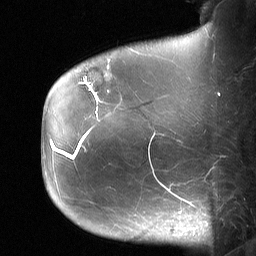
Breast MRI (dynamic contrast-enhanced), one sagittal slice; position 16 of 64 along the scan axis; dynamic contrast-enhanced study with each time point stored as its own series, time point 2 of 3 at this slice position (early post-contrast, ordered by acquisition time); 1.5 T; TE 4.8 ms, TR 27 ms; 256 × 256 image matrix, field of view 200 × 200 mm. Patient: female, 60 years. From the clinical record (not read from this slice): setting: breast cancer imaged before/during neoadjuvant chemotherapy; receptor status: HR-positive, HER2-negative.
Annotated regions visible in this slice (semi-automatically segmented with operator editing):
- analysis volume of interest (the breast-tissue region the enhancement analysis was run in; not a lesion): bounding box [x1, y1, x2, y2] px = [79, 50, 122, 99]
- tumour enhancement mask (voxels above the 90 % enhancement threshold inside the analysis volume of interest): [87, 83, 97, 98]